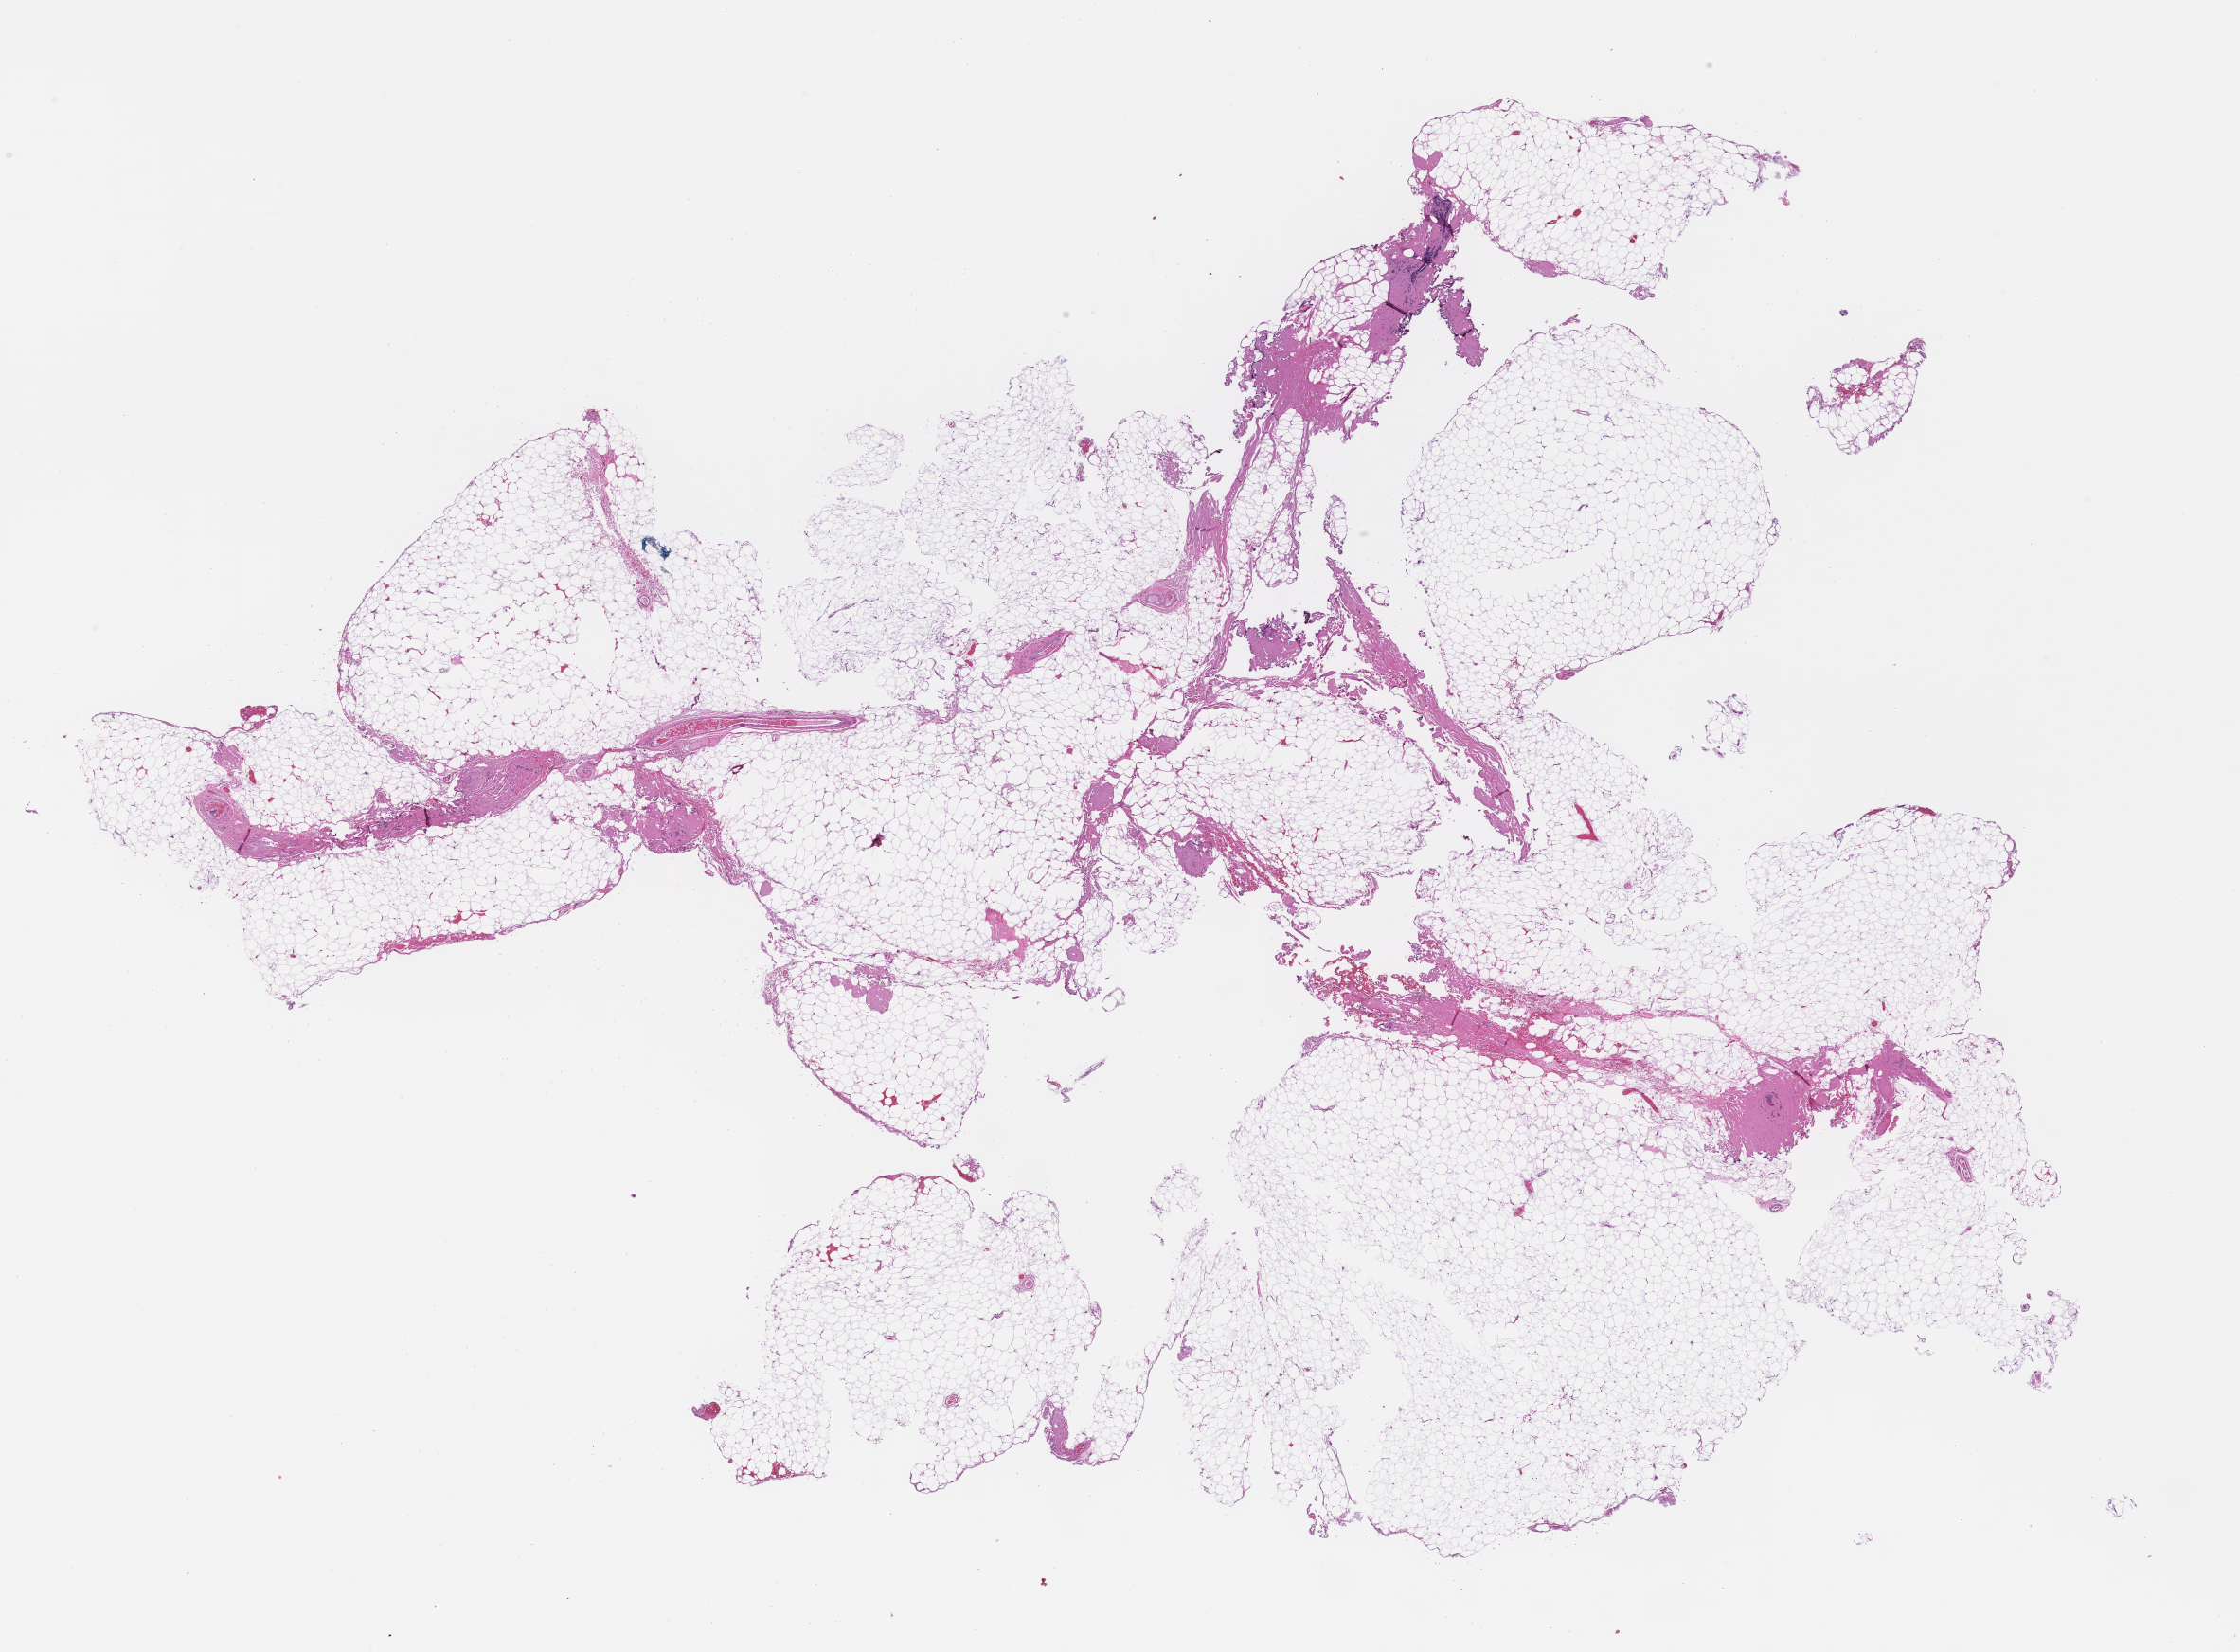
Hematoxylin and eosin (H&E) whole-slide image — a low-resolution overview of the entire scanned area, about 19.1 x 14.1 mm. Formalin-fixed, paraffin-embedded (FFPE) tissue. Site: breast. Specimen time point: collected post-treatment, no progression. Female patient.
This section: primary tumor. Diagnosis: Invasive Breast Carcinoma.